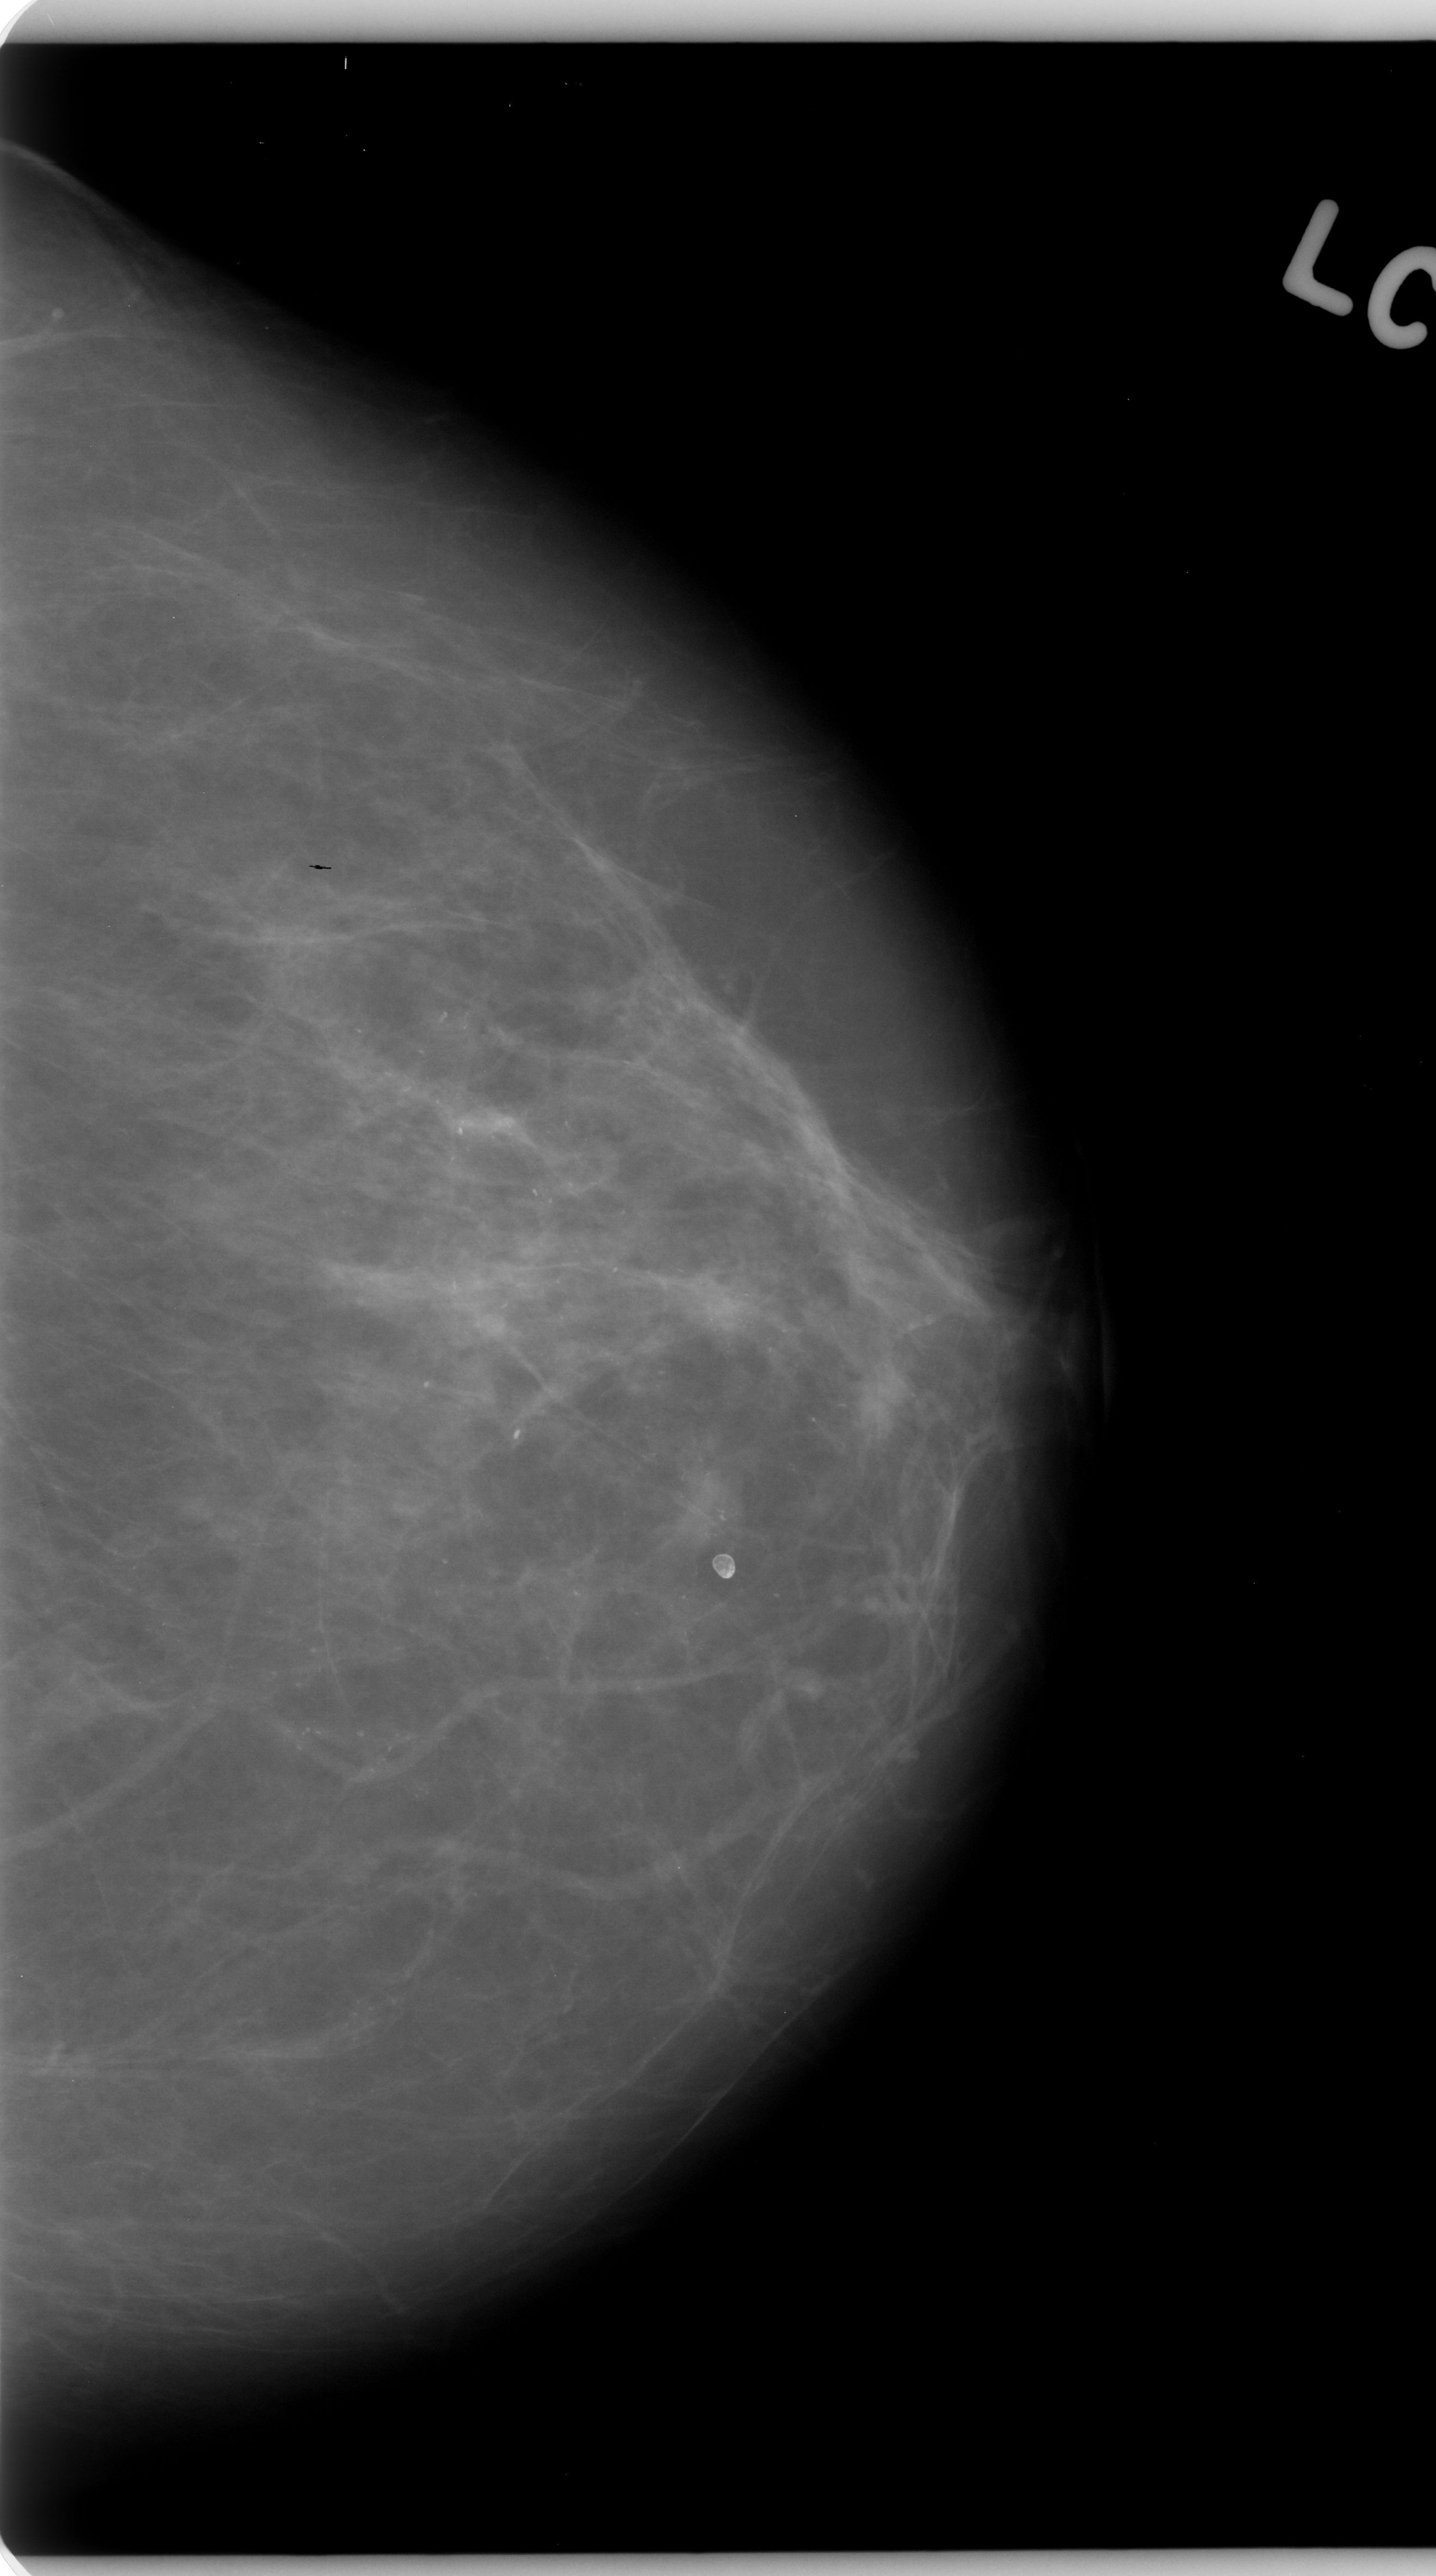
Digitized screen-film mammogram; left breast; craniocaudal (CC) view; BI-RADS breast density category 1 (scale 1–4).
- Calcifications, morphology amorphous, distribution regional; BI-RADS assessment category 5; pathology result (as recorded, not read from the image): malignant.